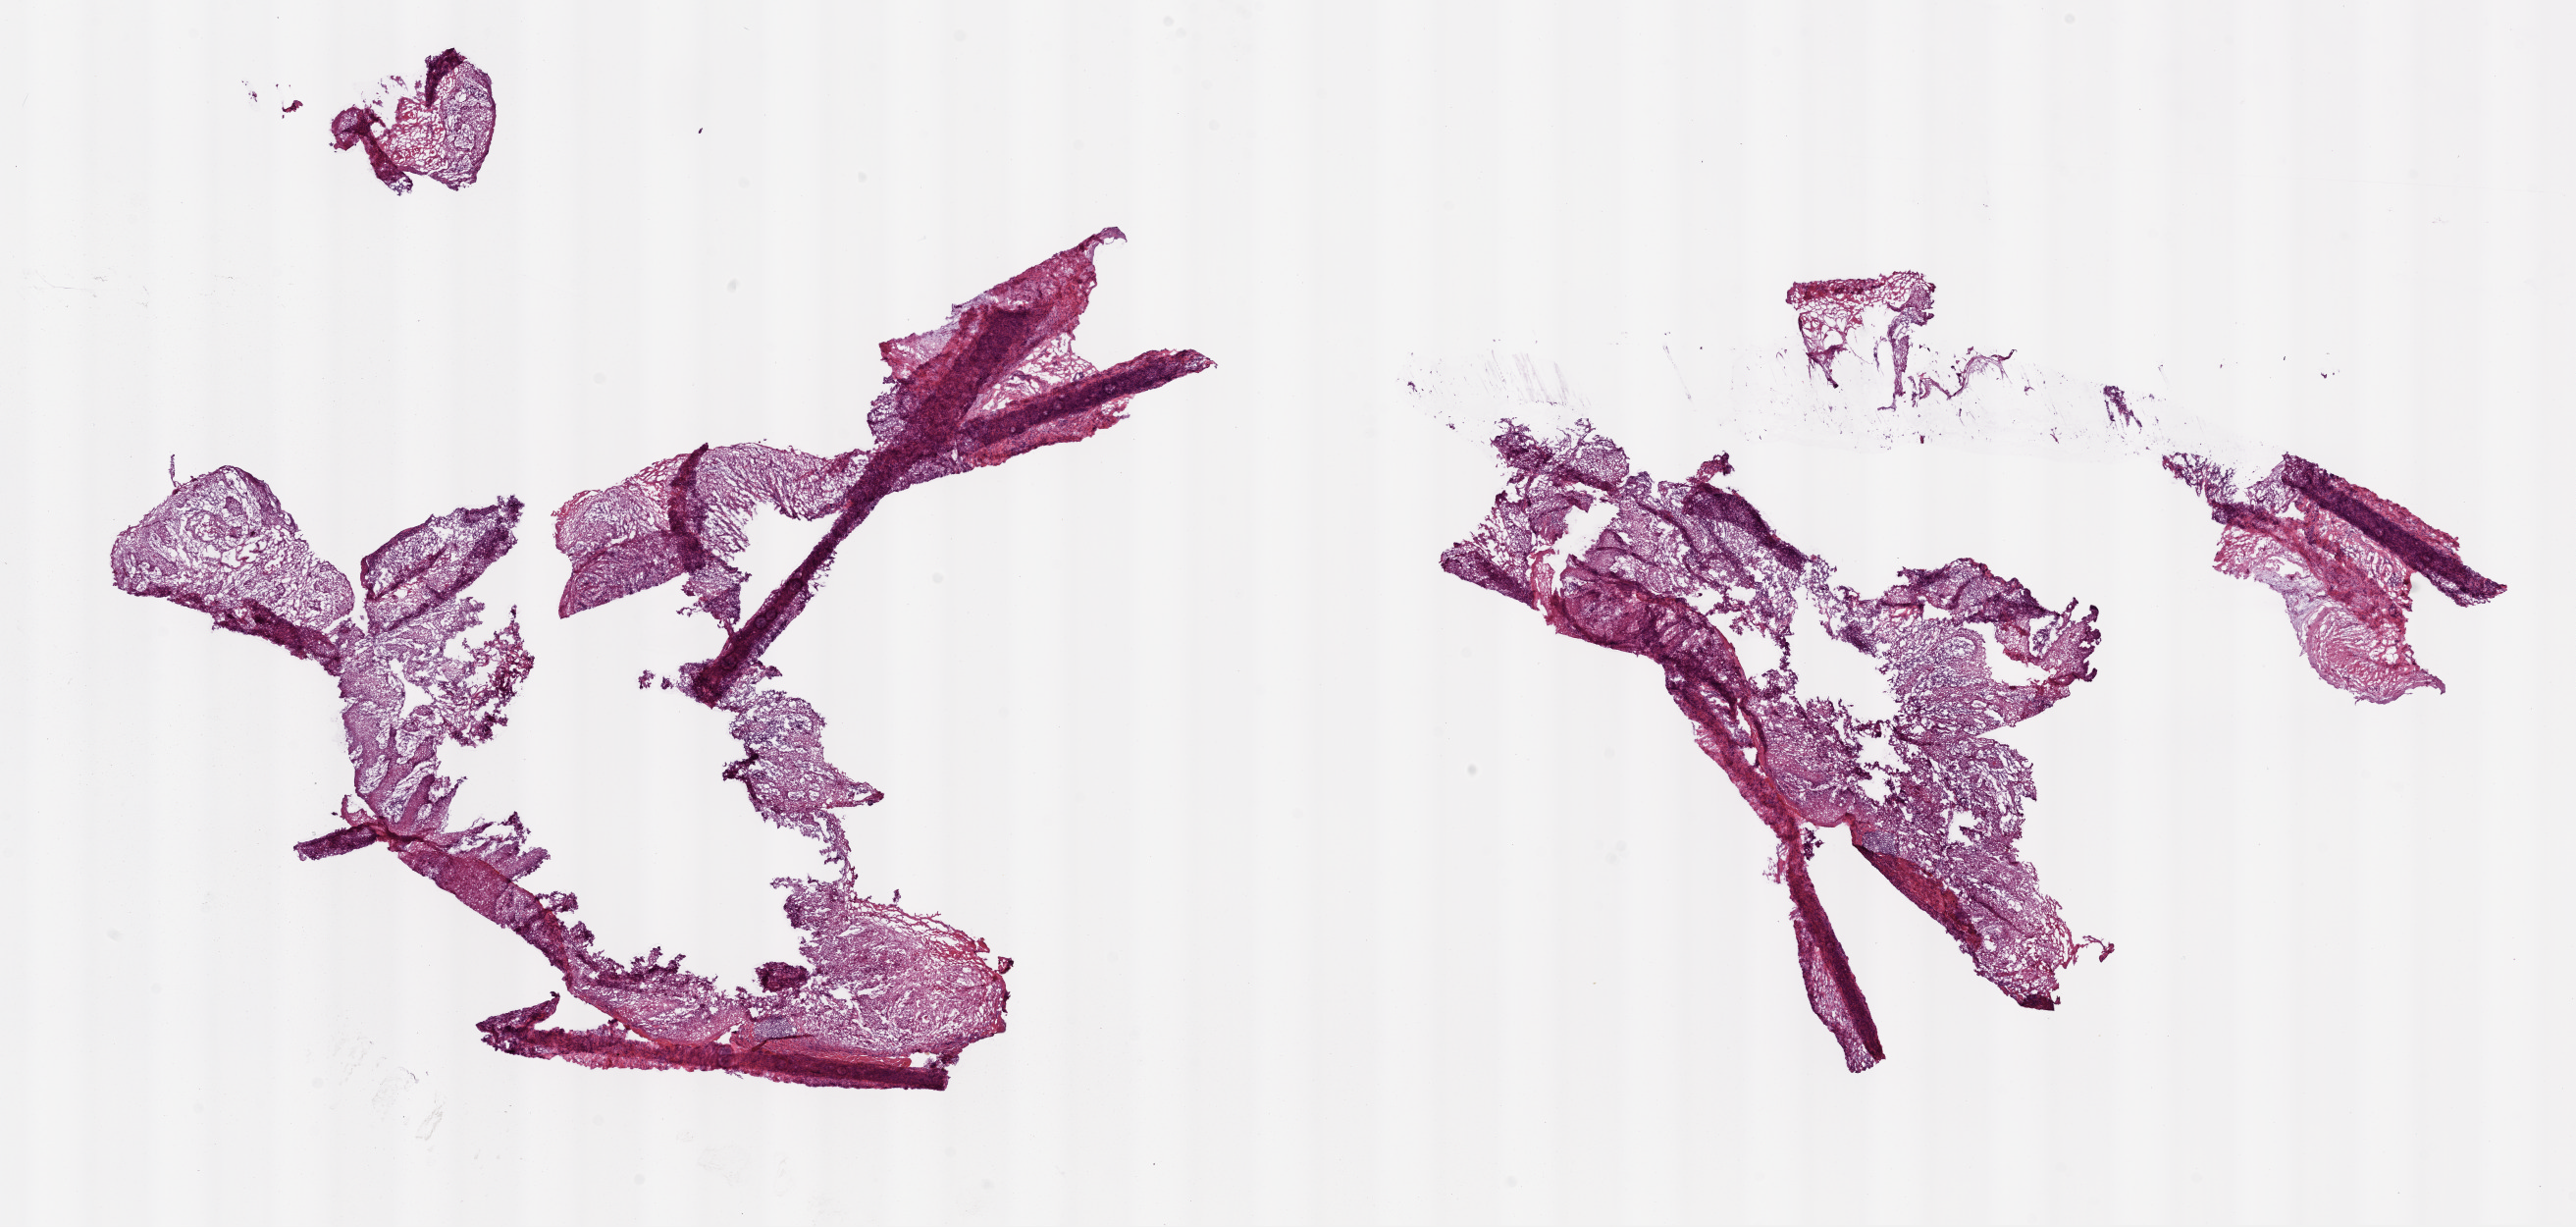
Digitized H&E tissue section (whole slide) — low-resolution overview of the scanned area, about 21.1 x 10.0 mm (slide scanned at 20x). Frozen section from the top of the tissue portion. Head and neck, primary tumour sample. Patient sex: female.
Pathologic diagnosis: Squamous cell carcinoma, NOS (hard palate).